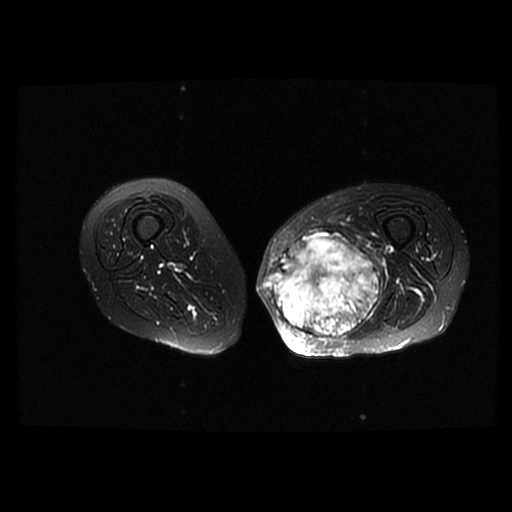
MRI of an extremity soft-tissue mass, one axial slice. T2-weighted fat-saturated. 6 mm slice thickness. 512 × 512 image matrix, field of view 420 × 420 mm. Female patient. Case-level facts recorded for this patient, not image findings: histological type: pleomorphic leiomyosarcoma; grade: high; site of the primary tumour: left thigh.
Outlined on this slice (expert manual segmentation):
- gross tumour volume including surrounding oedema: bounding box <263,230,380,338> (left, top, right, bottom; pixels)
- gross tumour volume (mass): <263,230,380,338>